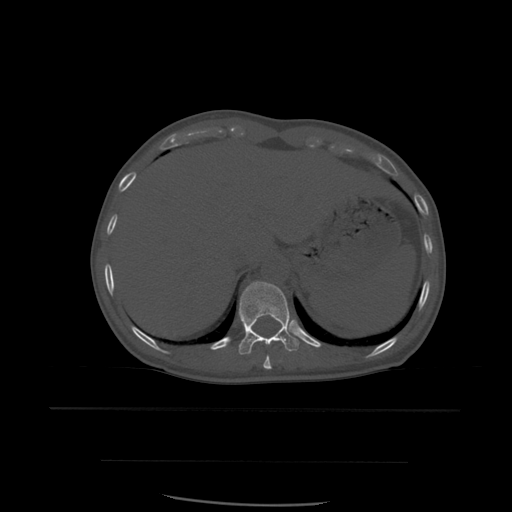
CT including the spine, one axial slice. Bone window (W 1800 / L 400 HU). 1.25 mm slice thickness. 512 × 512 image matrix, field of view 392 × 392 mm. Patient age 48 years. From the clinical record (not read from this slice): primary cancer: lung; vertebrae with lytic lesions (as recorded): T11.
Annotated regions visible in this slice (semi-automatically segmented with operator editing):
- T10 vertebra: bounding box (x1, y1, x2, y2) in pixels: (263, 349, 287, 370)
- T11 vertebra: (239, 282, 300, 355)